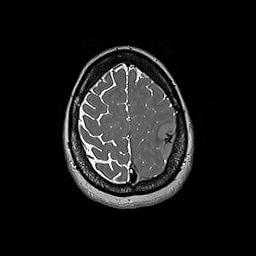
Brain MRI from a brain-tumour surgery series, one axial slice. Position 53 of 192 along the scan axis. 1 mm slice thickness. 256 × 256 image matrix, field of view 250 × 250 mm. Case-level facts recorded for this patient, not image findings: histopathology: Glioblastoma; WHO grade: 4; IDH mutation: no; tumour location: Left Frontal.
Outlined on this slice (expert manual segmentation):
- tumour: bounding box <159,123,182,163> (left, top, right, bottom; pixels)